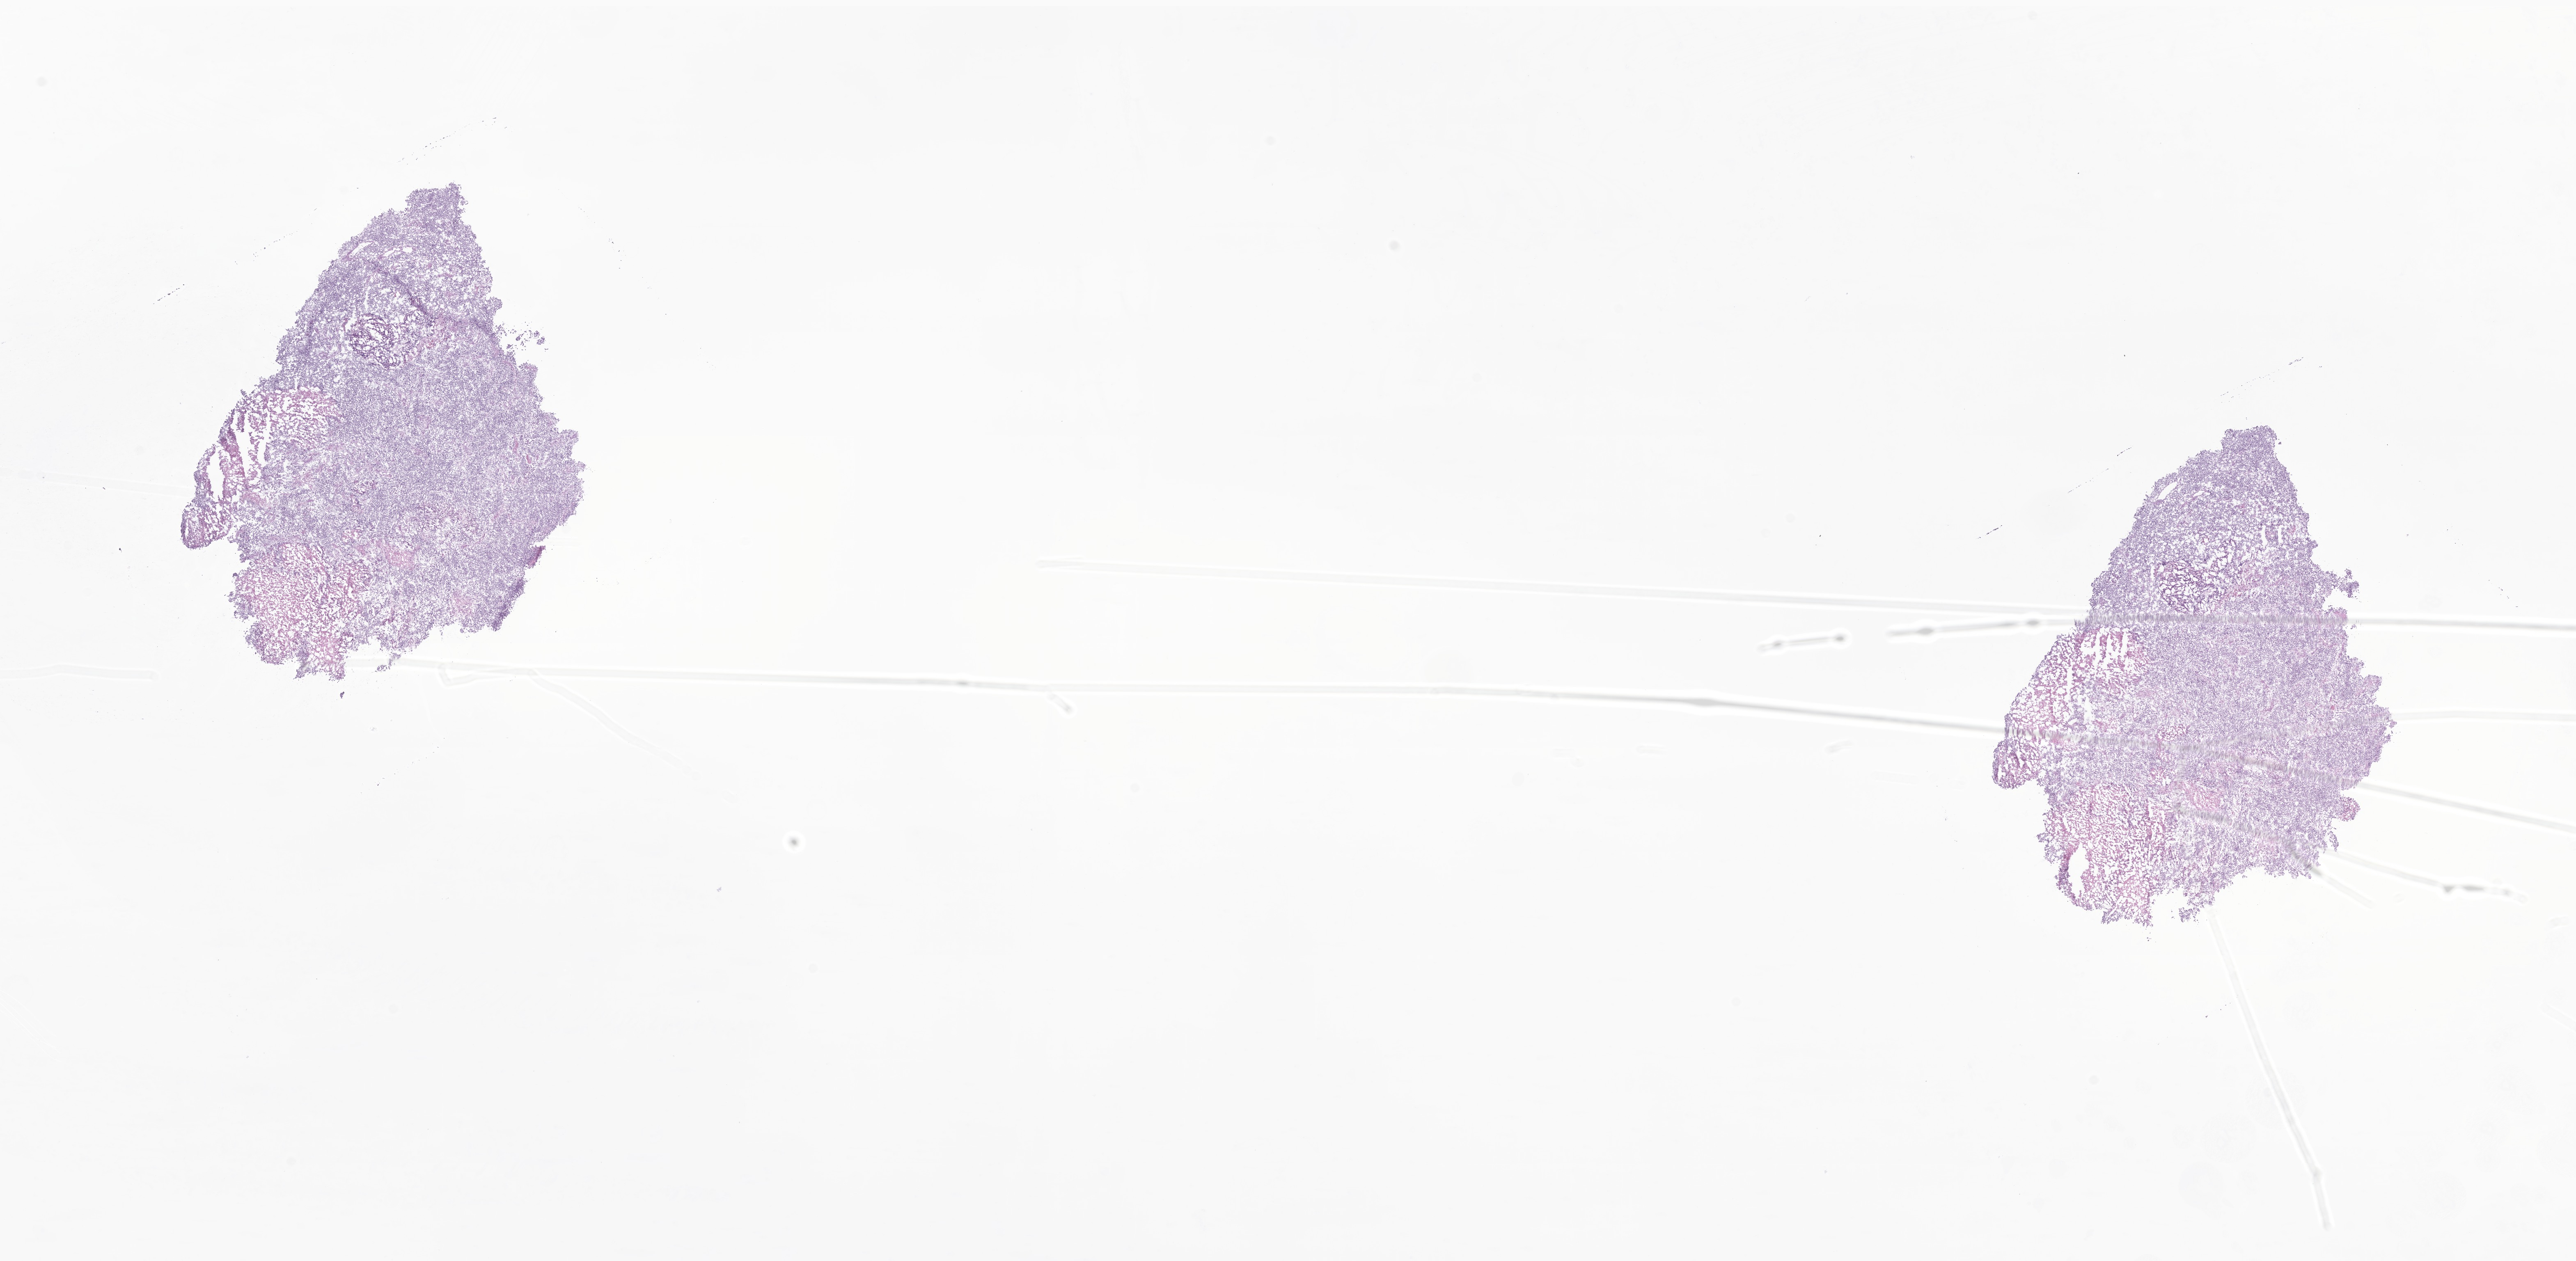
Whole-slide image, hematoxylin and eosin (H&E) stain of tumor tissue from the brain — whole scanned area (about 26.5 x 13.0 mm) shown as a low-resolution overview; cryosection (OCT / tissue freezing medium). Patient male; age 49 months.
• diagnosis: Glioma, malignant